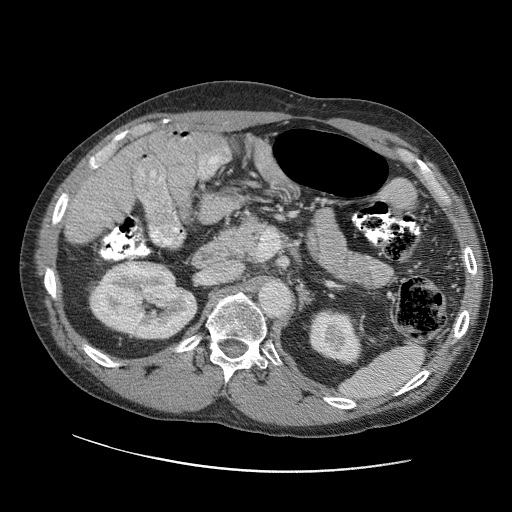
Contrast-enhanced abdominal CT (liver protocol), one axial slice; slice 51 of 109 in the series (ordered by position); reconstruction kernel STANDARD; 120 kVp; soft-tissue window (W 400 / L 40 HU); 2.5 mm slice thickness; 512 × 512 image matrix, field of view 400 × 400 mm. From the clinical record (not read from this slice): diagnosis: hepatocellular carcinoma (patient treated with transarterial chemoembolisation; whether this scan precedes or follows treatment is not stated here); TNM stage (as recorded): Stage-IIIC; Child-Pugh class: B; tumour differentiation: well differentiated; tumour nodularity: uninodular.
Outlined on this slice (semi-automatic segmentation, software-assisted and operator-edited):
- liver parenchyma outside the tumour (the mass and vessels are separate outlines, so this box may not span the whole liver): box from (x=114, y=132) to (x=210, y=166) px
- liver vessels: (x=123, y=135)–(x=200, y=164)